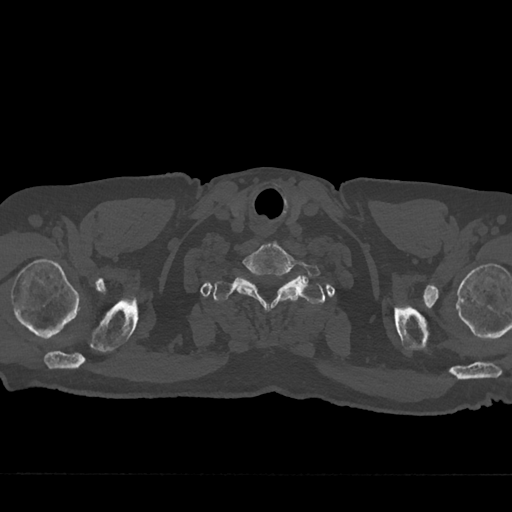
CT including the spine, one axial slice; position 679 of 797 along the scan axis; 120 kVp; bone window (W 1800 / L 400 HU); 0.5 mm slice thickness; 512 × 512 image matrix. Patient: male, 75 years. Case-level facts recorded for this patient, not image findings: primary cancer: renal.
Annotated regions visible in this slice (semi-automatically segmented with operator editing):
- T1 vertebra: bounding box <213,277,324,304> (left, top, right, bottom; pixels)